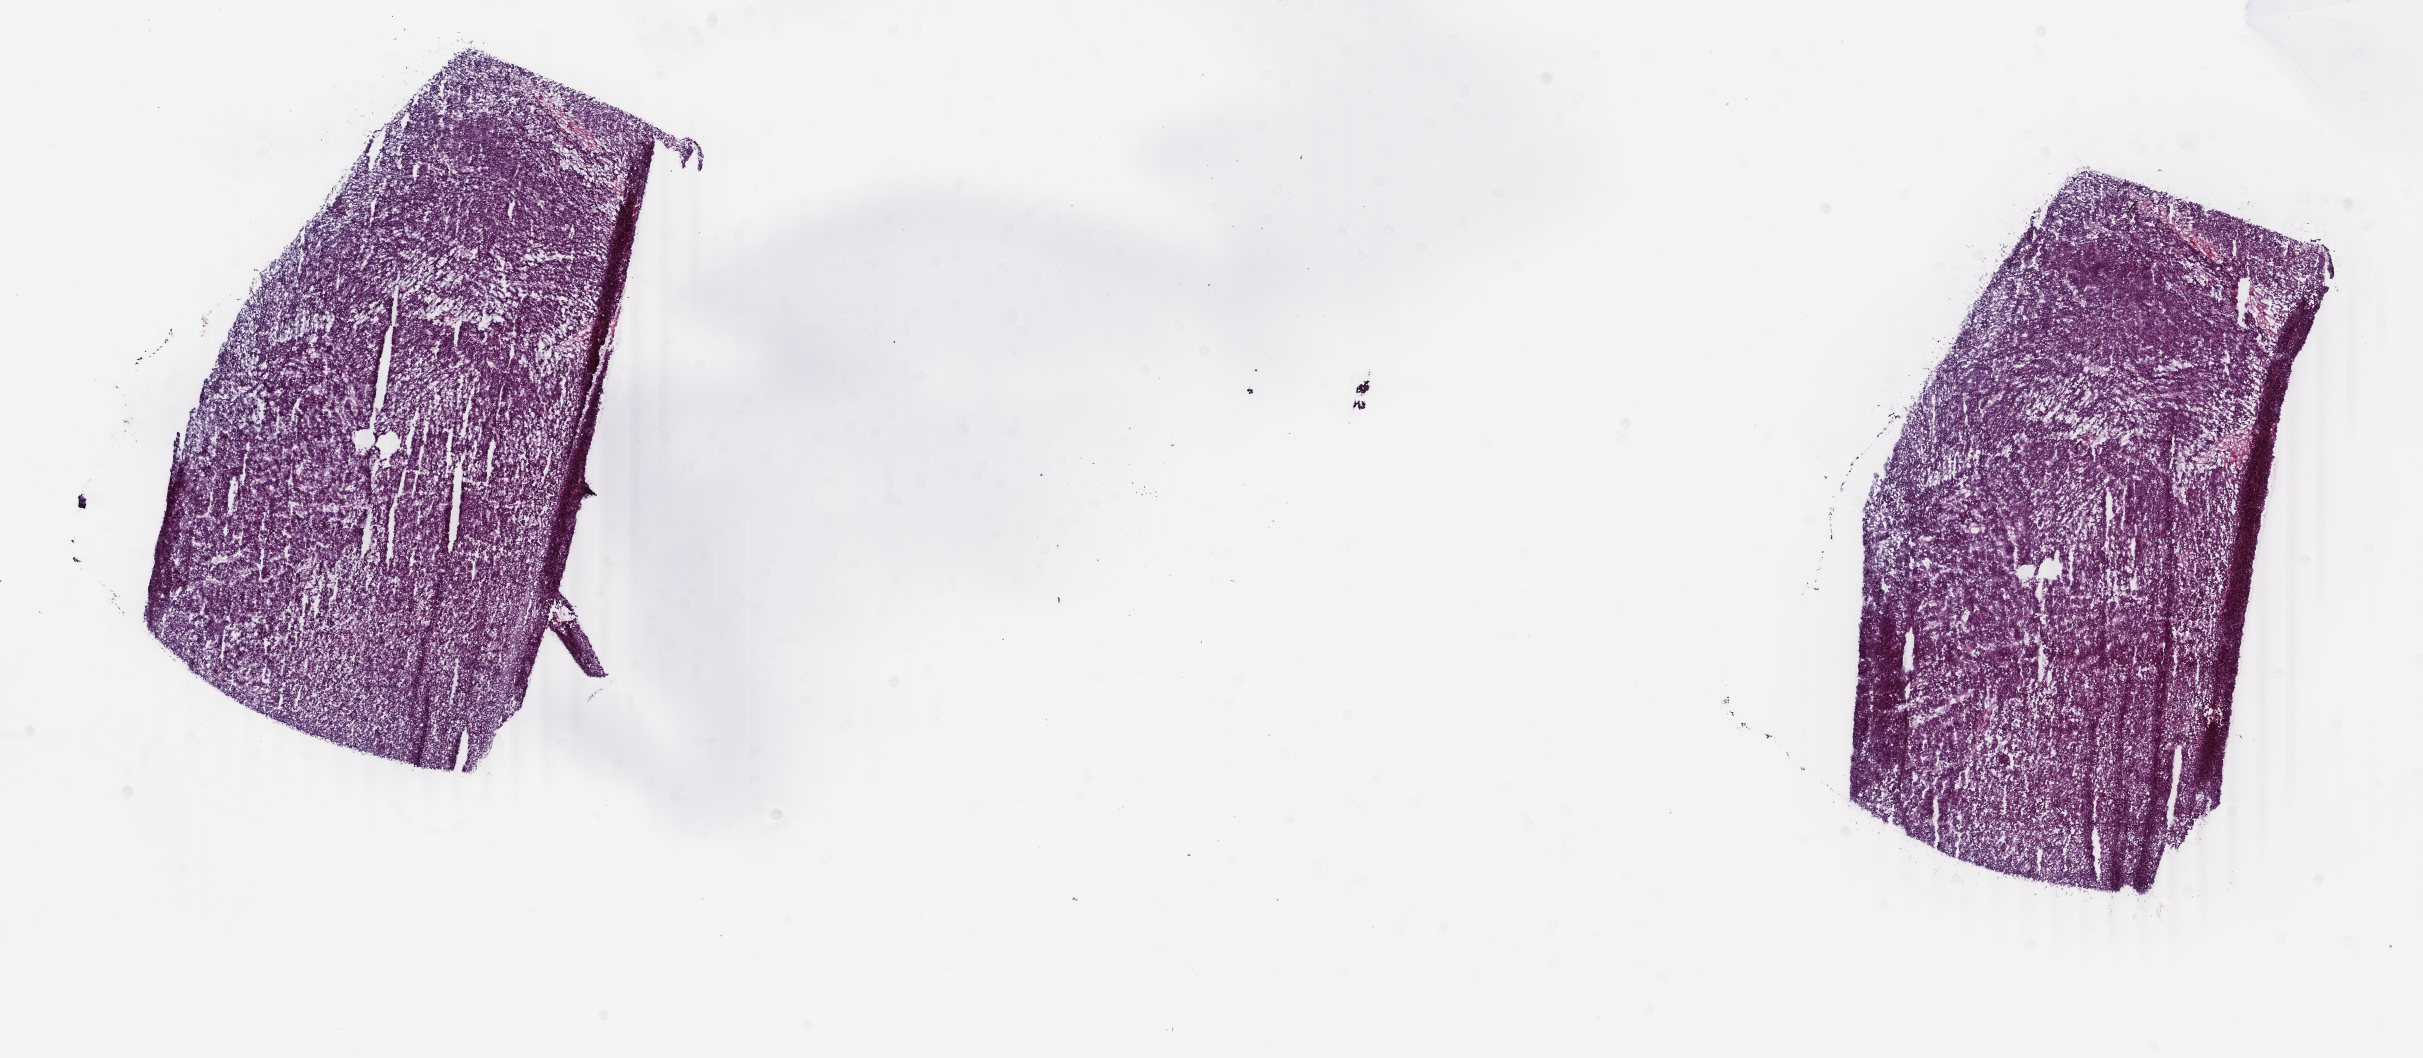
Whole-slide histology image, Hematoxylin and eosin (H&E) stained, a low-resolution overview of the entire scanned area, about 19.3 x 8.4 mm, frozen section from the top of the tissue portion, sample: primary tumour, liver. Female, age 62 years at initial diagnosis. Histologic grade: G2 (moderately differentiated). Composition of this section per pathologist review: tumour cells 80%, tumour nuclei 85%, normal cells 0%, stromal cells 15%, necrosis 5%. Infiltration values recorded for this section: lymphocyte infiltration 3%, monocyte infiltration 0%, neutrophil infiltration 0%.
Histologic diagnosis: Hepatocellular carcinoma, NOS. AJCC pathologic stage: I.